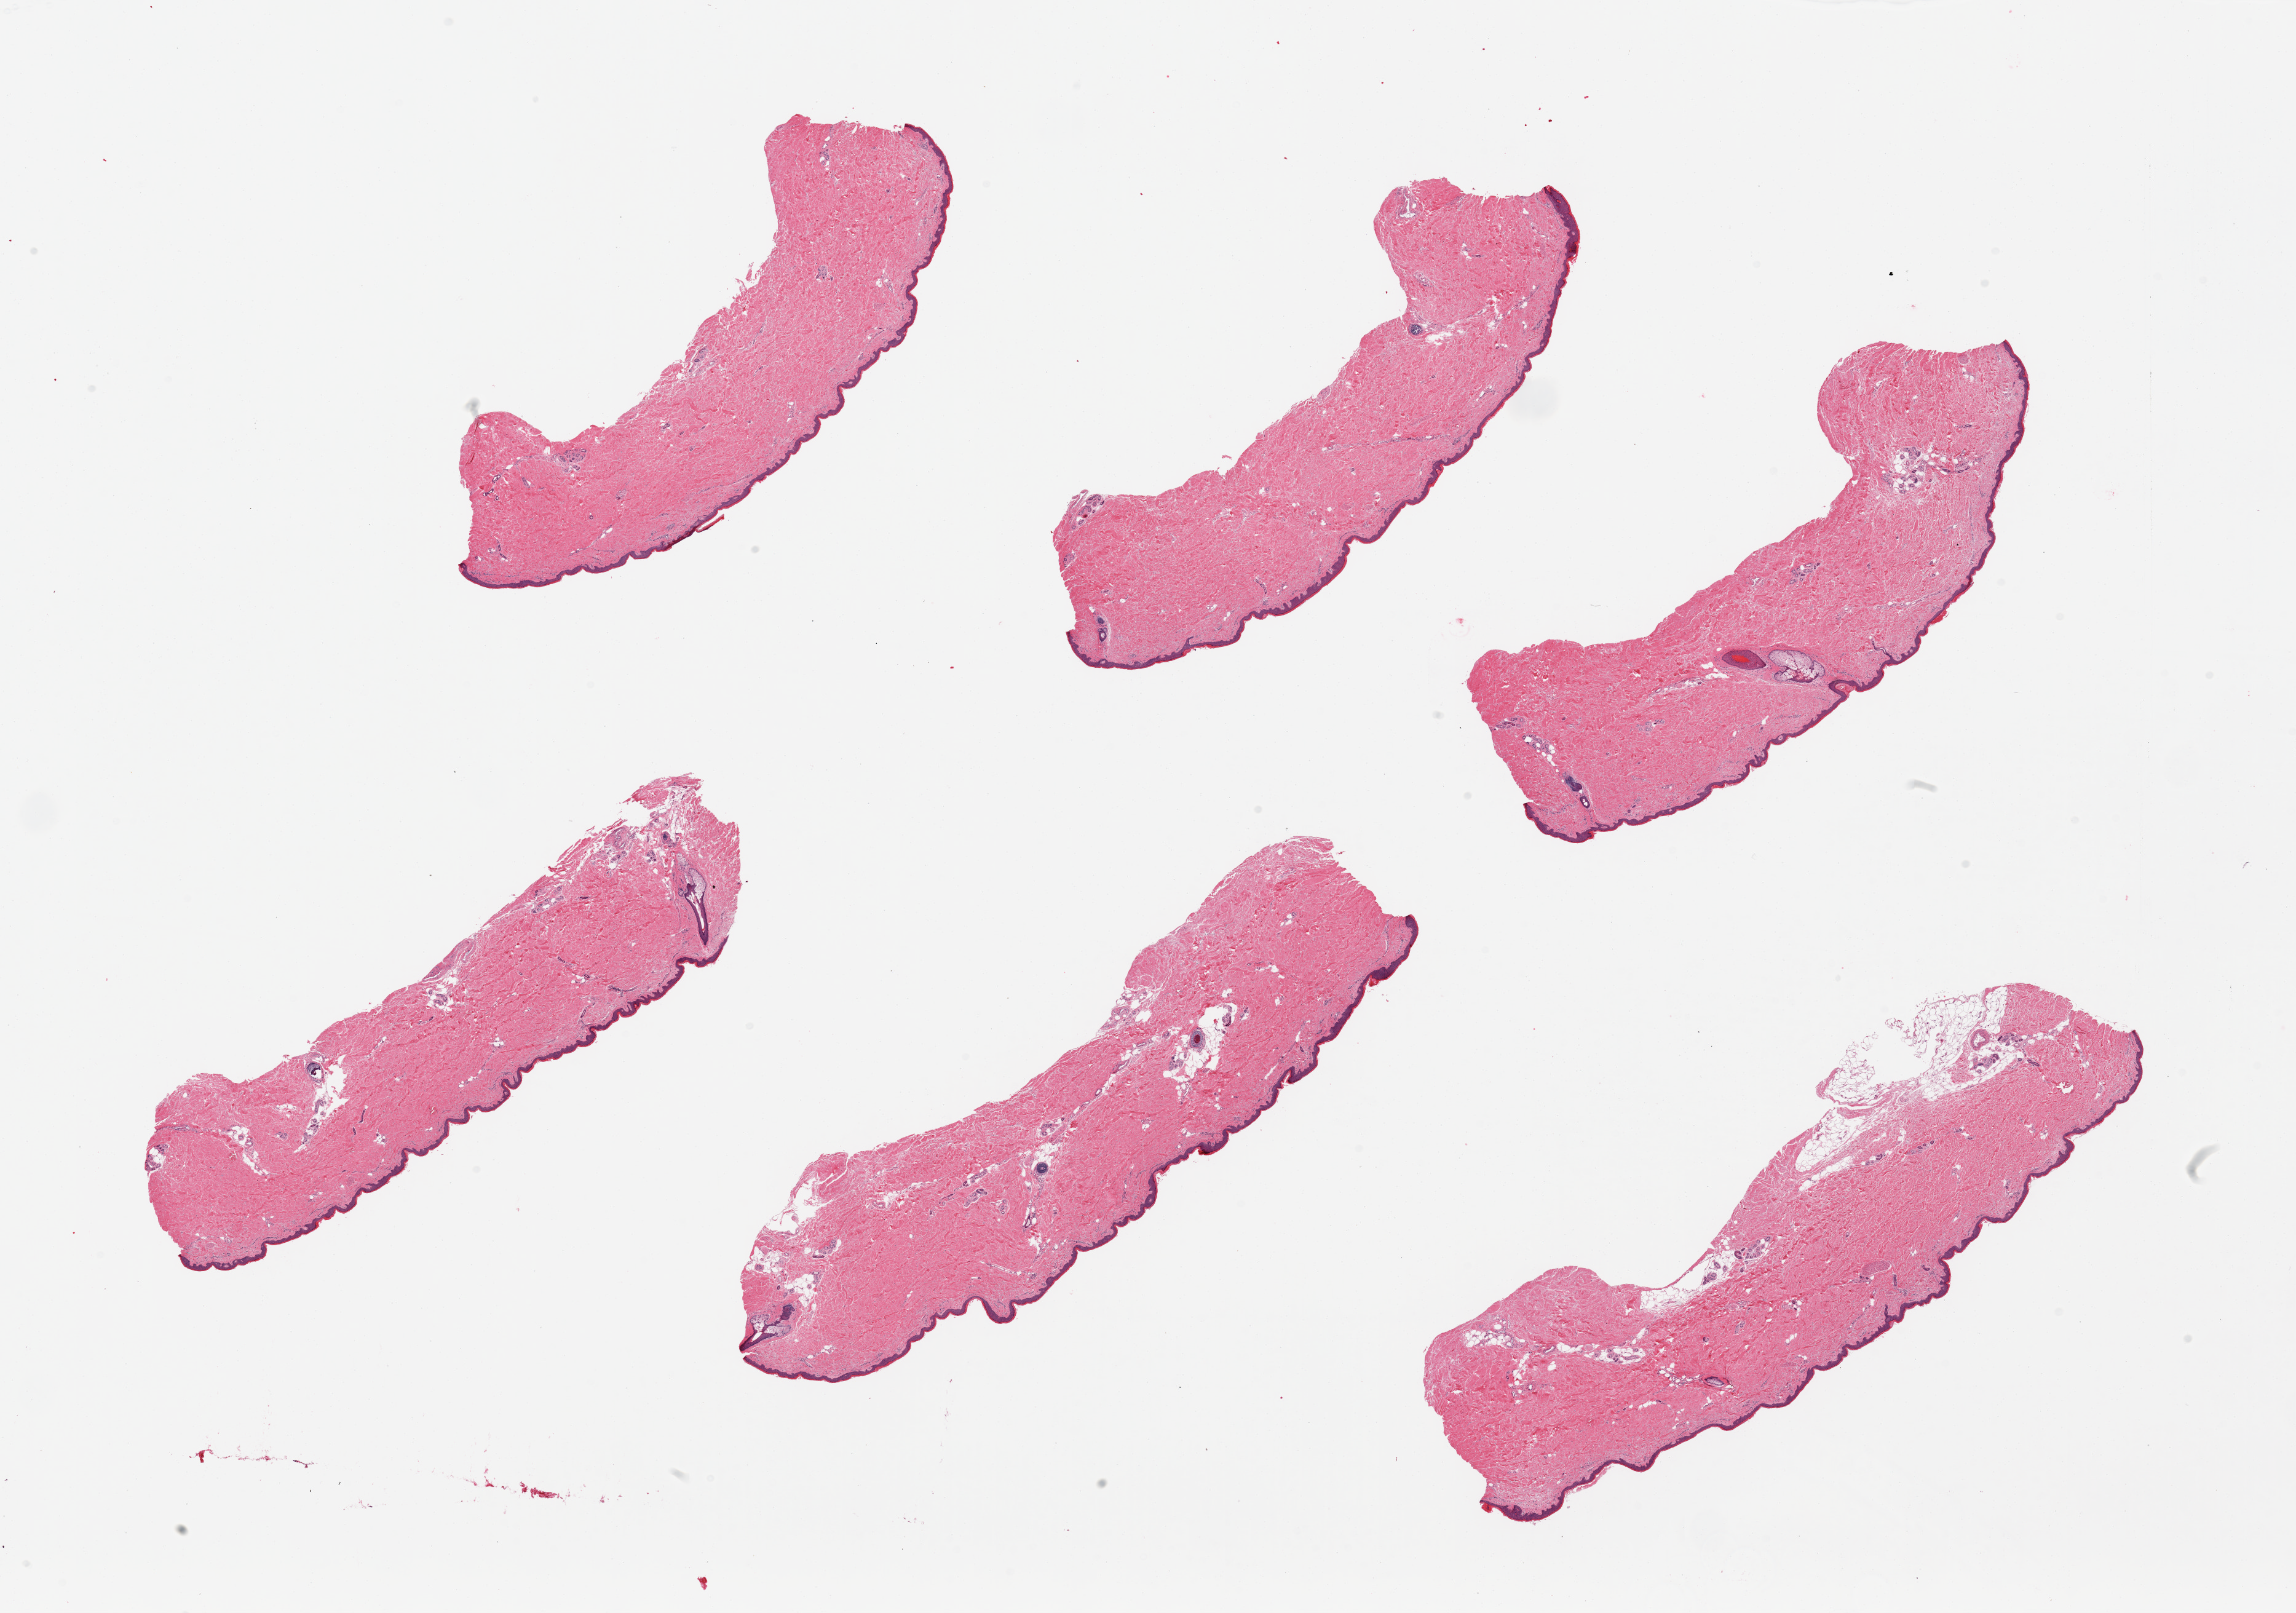
Whole-slide image, hematoxylin and eosin (H&E) stain, shown as a low-resolution overview of the whole scanned area (about 29.5 x 20.7 mm), PAXgene-fixed, paraffin-embedded tissue, target tissue: skin of lower leg, donor tissue sample. Male donor.
Review note (as recorded): 6 pieces, minimal dermal fat; squamous epithelium is ~50 microns.